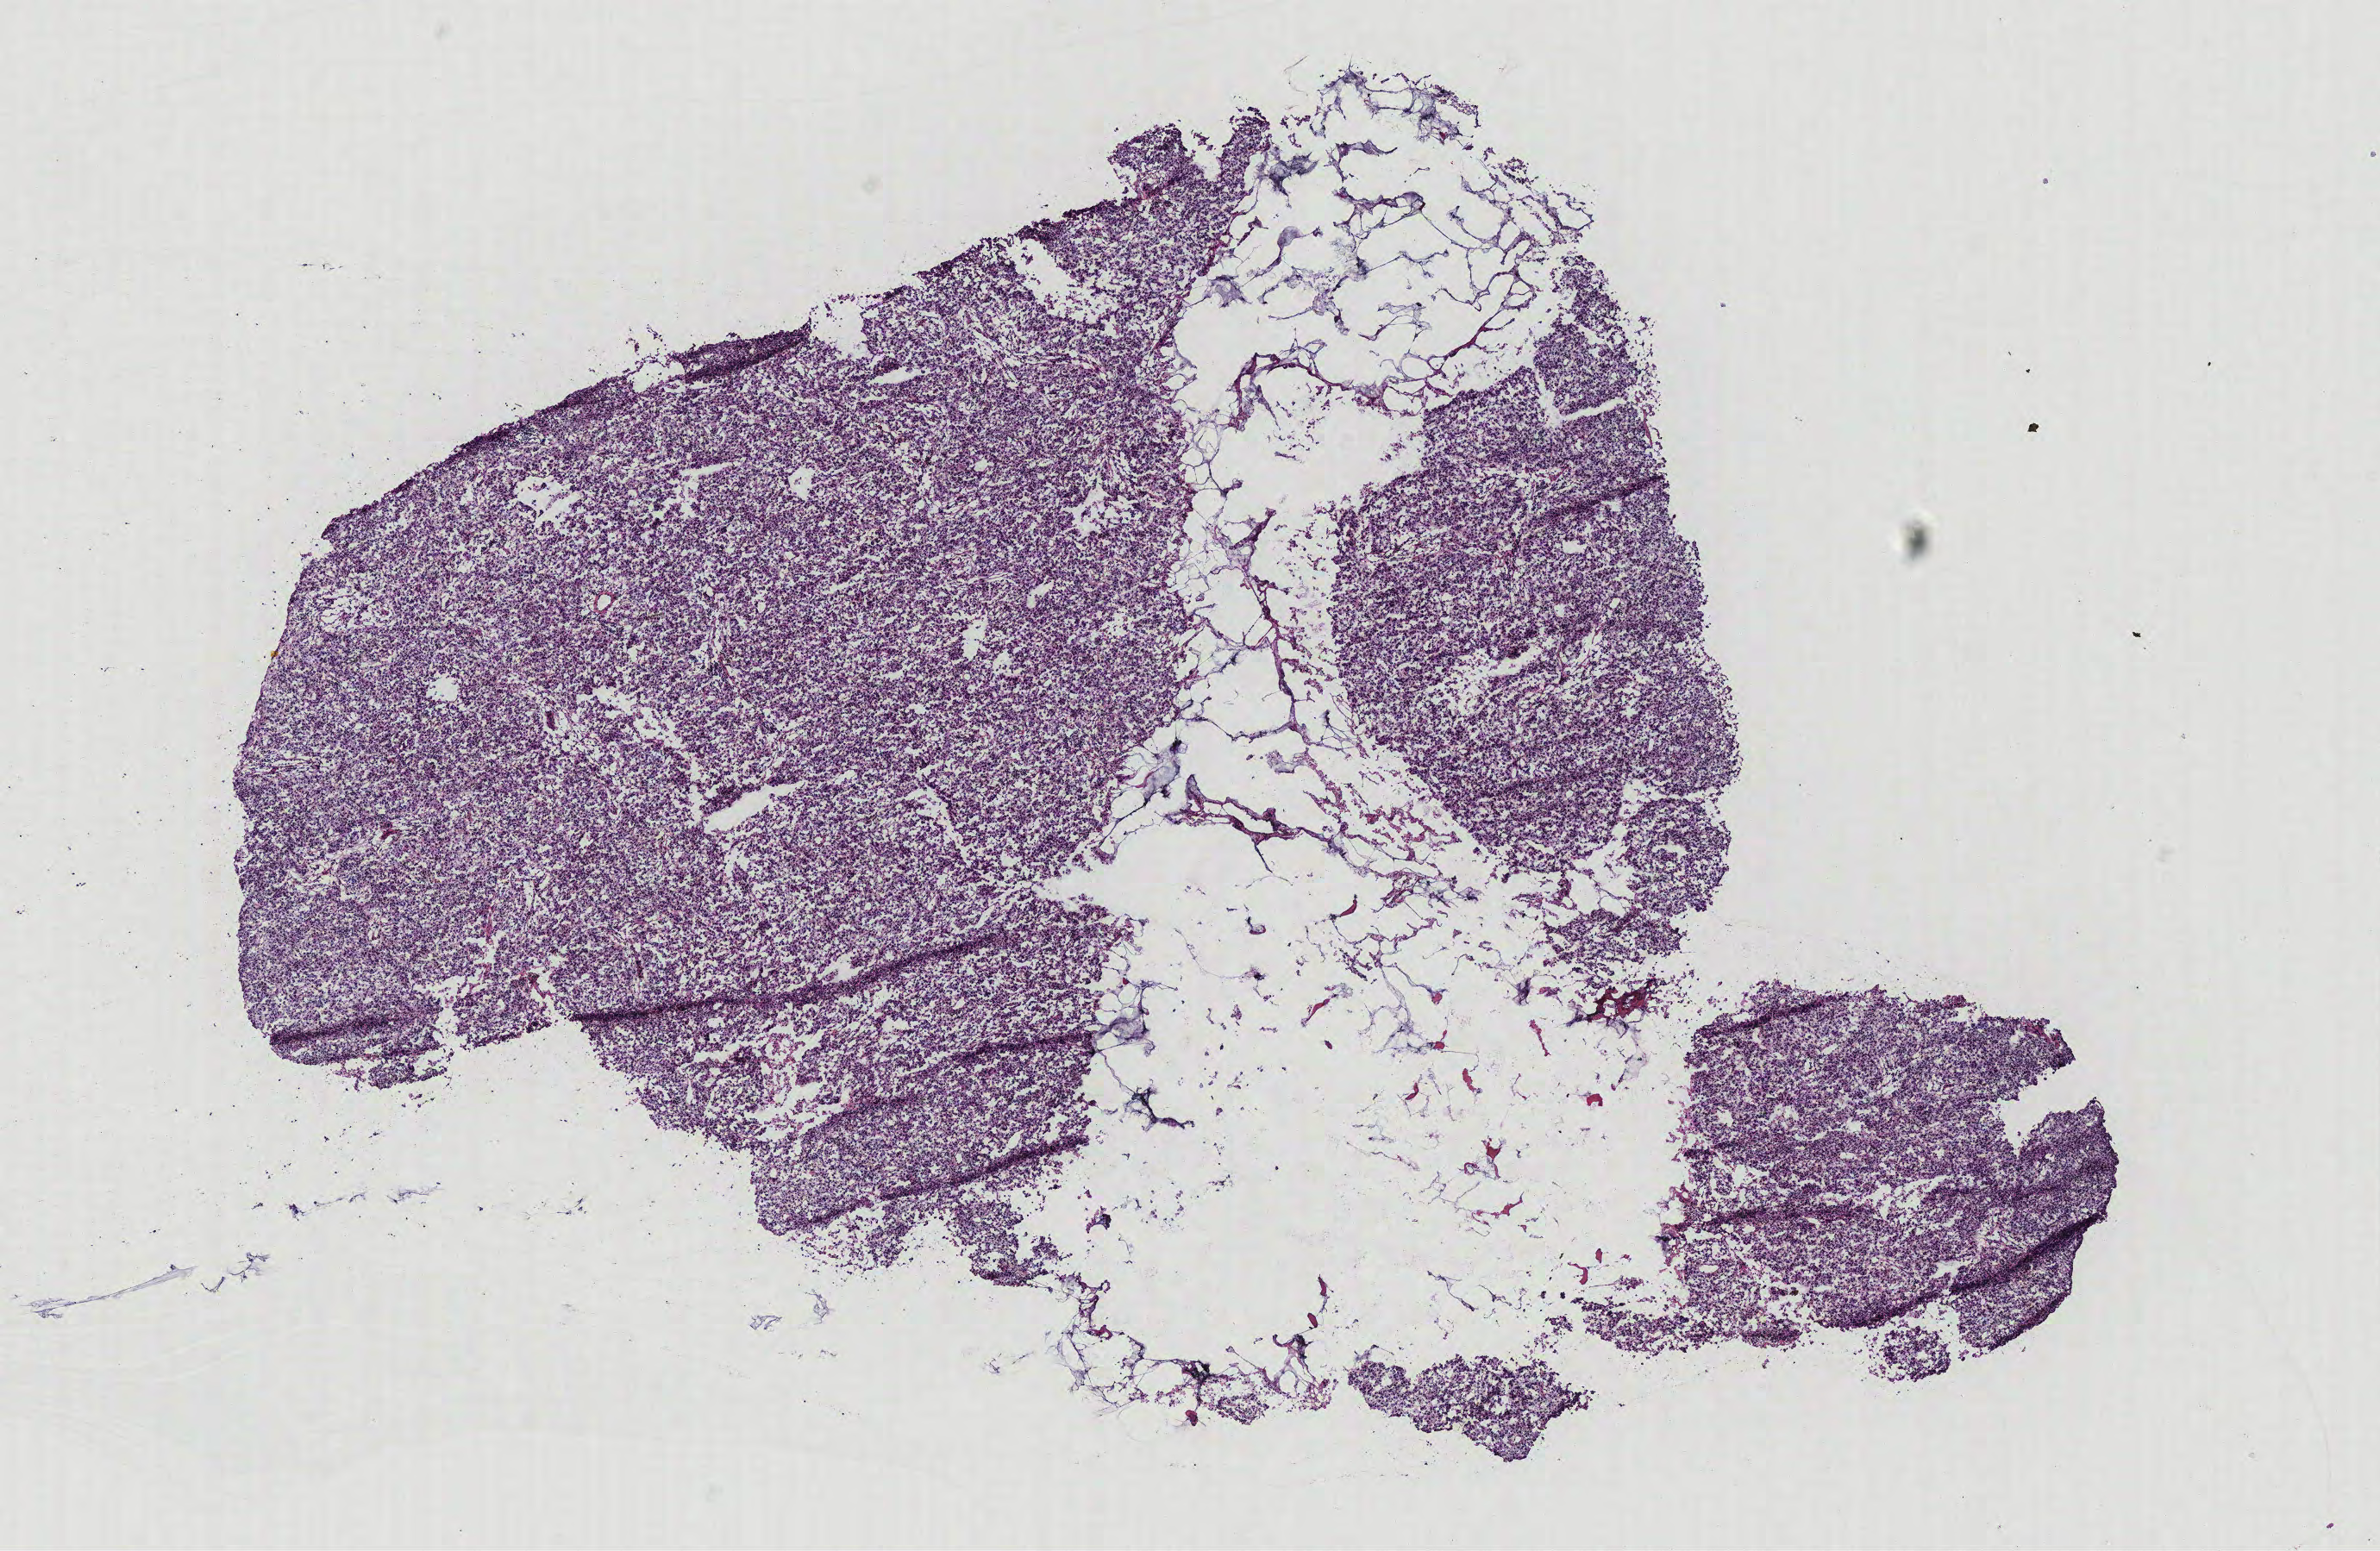
Whole-slide histology image, H&E, low-resolution overview of the scanned area, about 11.0 x 7.2 mm (from a 40x scan). Breast, tissue type not recorded. Female, 61 y/o.
Patient diagnosis: Infiltrating duct carcinoma, NOS.